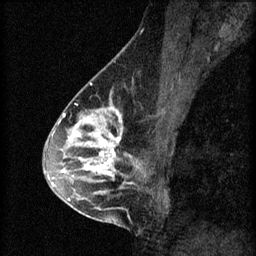
Breast MRI (dynamic contrast-enhanced), one sagittal slice. Slice 33 of 60 in the series (ordered by position). 3 images stored at this slice position (order not interpretable as contrast timing). 1.5 T. TE 4.2 ms, TR 8.2 ms. 2 mm slice thickness. 256 × 256 image matrix. Patient: female, 45 years.
Structures marked on this image (semi-automatically segmented with operator editing):
- analysis volume of interest (the breast-tissue region the enhancement analysis was run in; not a lesion): box from (x=54, y=104) to (x=159, y=217) px
- tumour enhancement mask (voxels above the 70 % enhancement threshold inside the analysis volume of interest): (x=54, y=104)–(x=147, y=201)